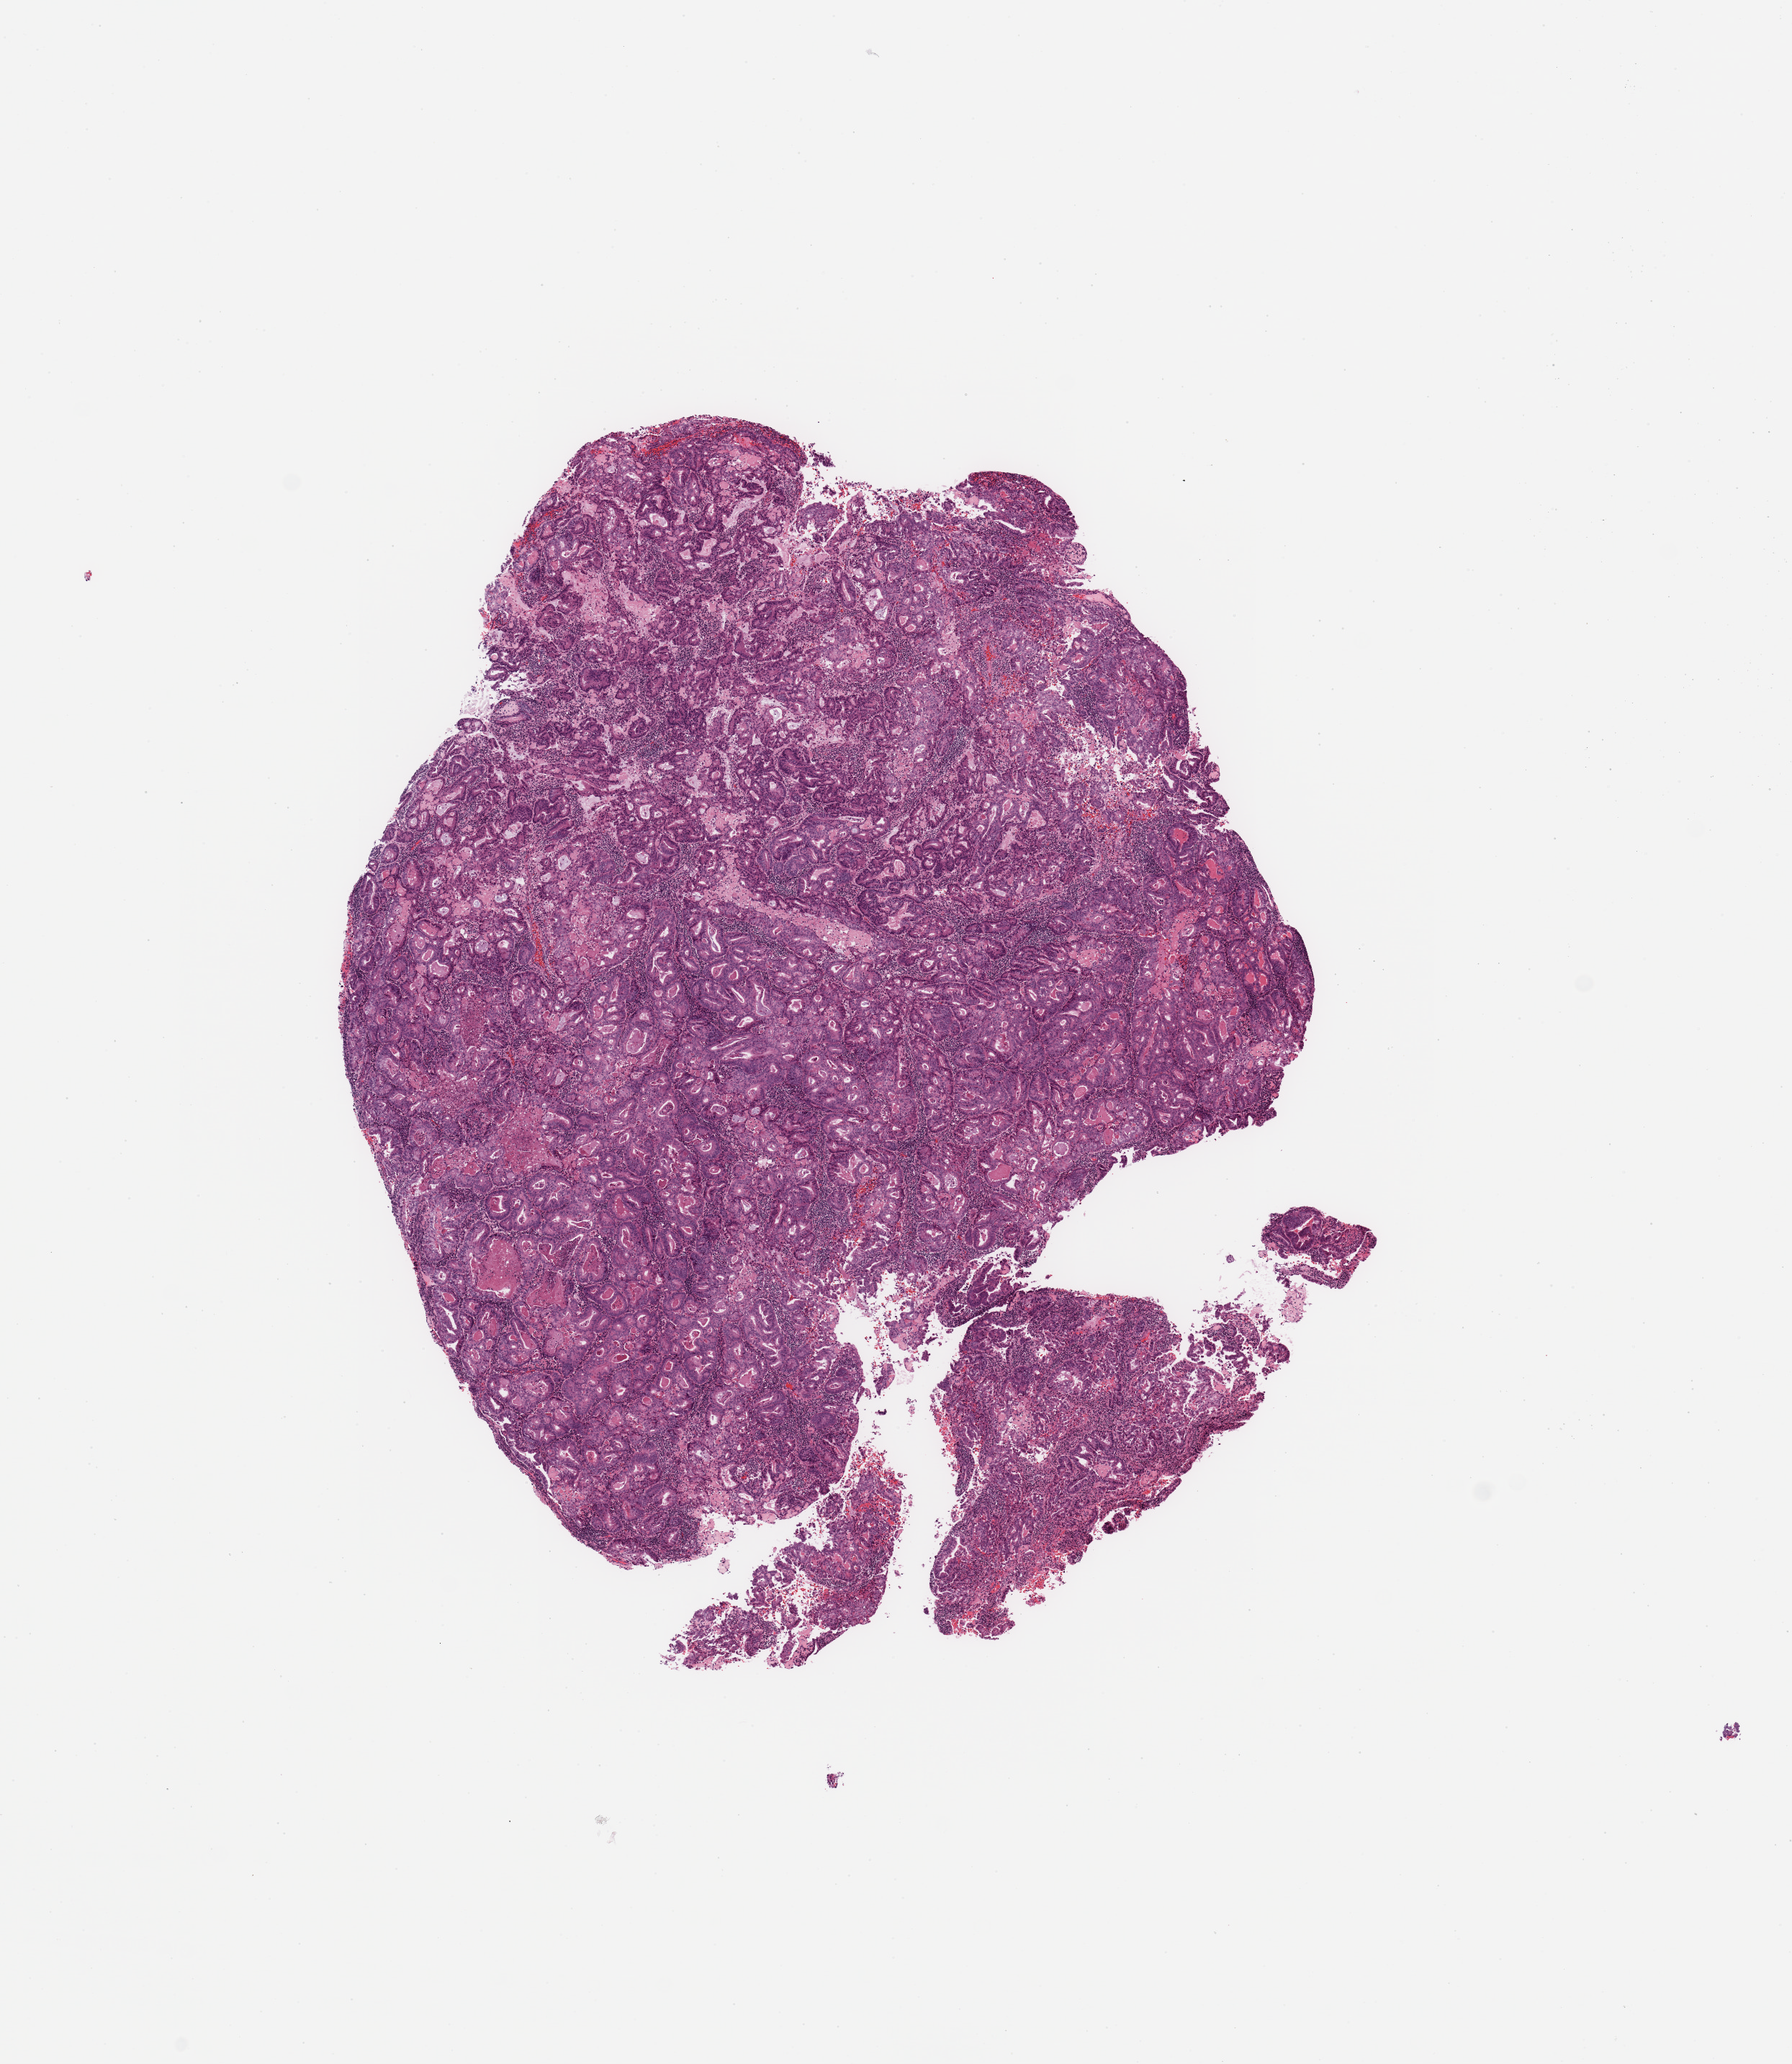
Digitized H&E-stained tissue section (whole slide) — whole scanned area (about 9.8 x 11.3 mm, slide scanned at 20x) shown as a low-resolution overview; tumour tissue sample, sampled site: uterus. 74-year-old female patient. Histologic grade: G3 (poorly differentiated). Composition of this section per pathologist review: tumour nuclei 90%, necrosis 2%.
Histologic diagnosis: Endometrioid adenocarcinoma, NOS. AJCC pathologic stage: IV.